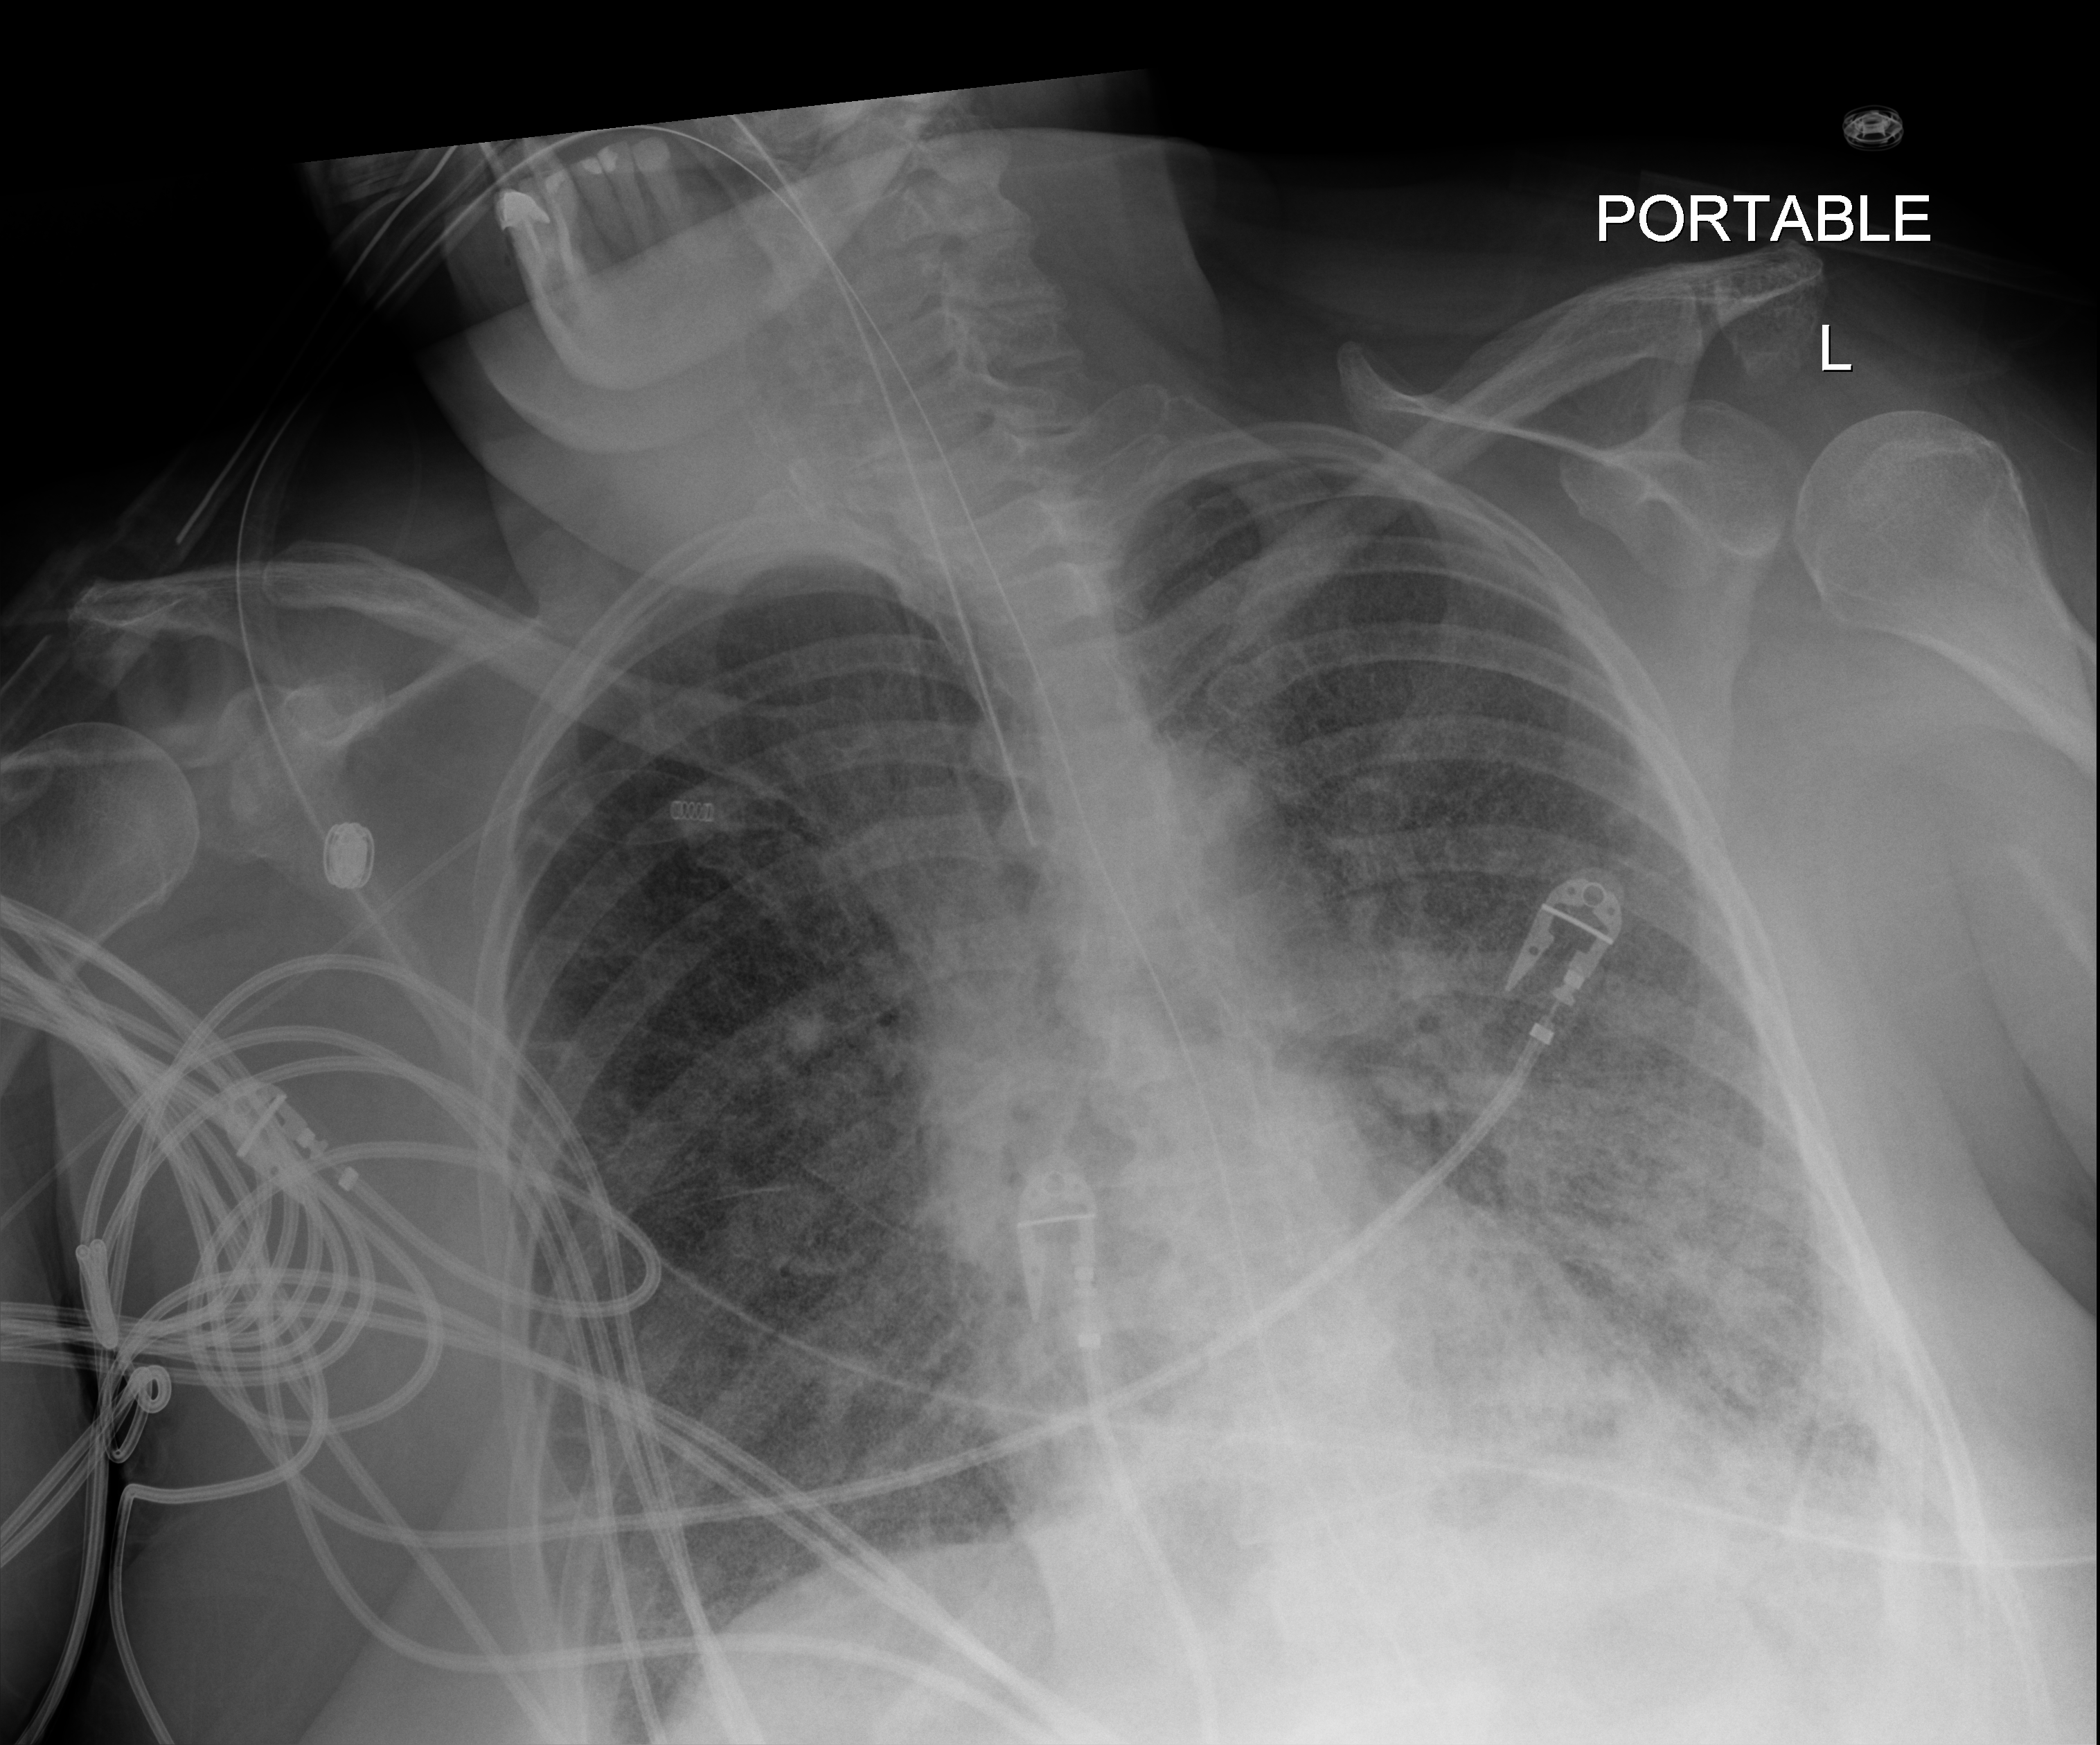
Bedside chest radiograph (digital radiography); anteroposterior (AP) projection. Patient hospitalised with COVID-19; female, aged 60–74 years.
Hospital-stay facts (about this admission, not read from this image; timing relative to this image not recorded):
- hypertension (admission record): no